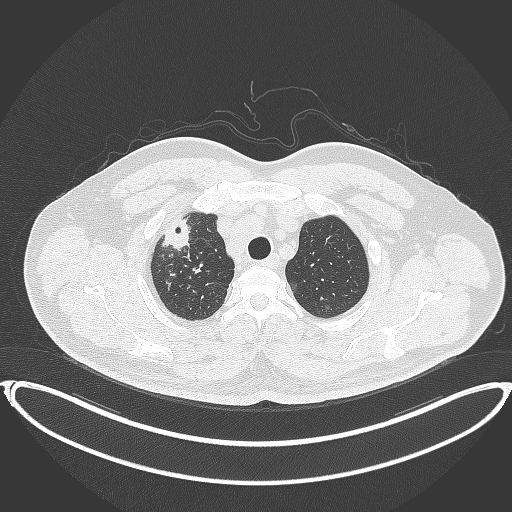
Chest CT, one axial slice. Slice 334 of 399 in the series (ordered by position). Reconstruction kernel B70f. 120 kVp. Lung window (W 1500 / L -600 HU). 512 × 512 image matrix, field of view 445 × 445 mm. Male patient, age 53 years. From the clinical record (not read from this slice): clinical TNM (as recorded): T2a N0 M0.
Structures marked on this image (rectangle marked by the reading radiologist):
- lung tumour (recorded histology: adenocarcinoma): box from (x=158, y=212) to (x=193, y=253) px